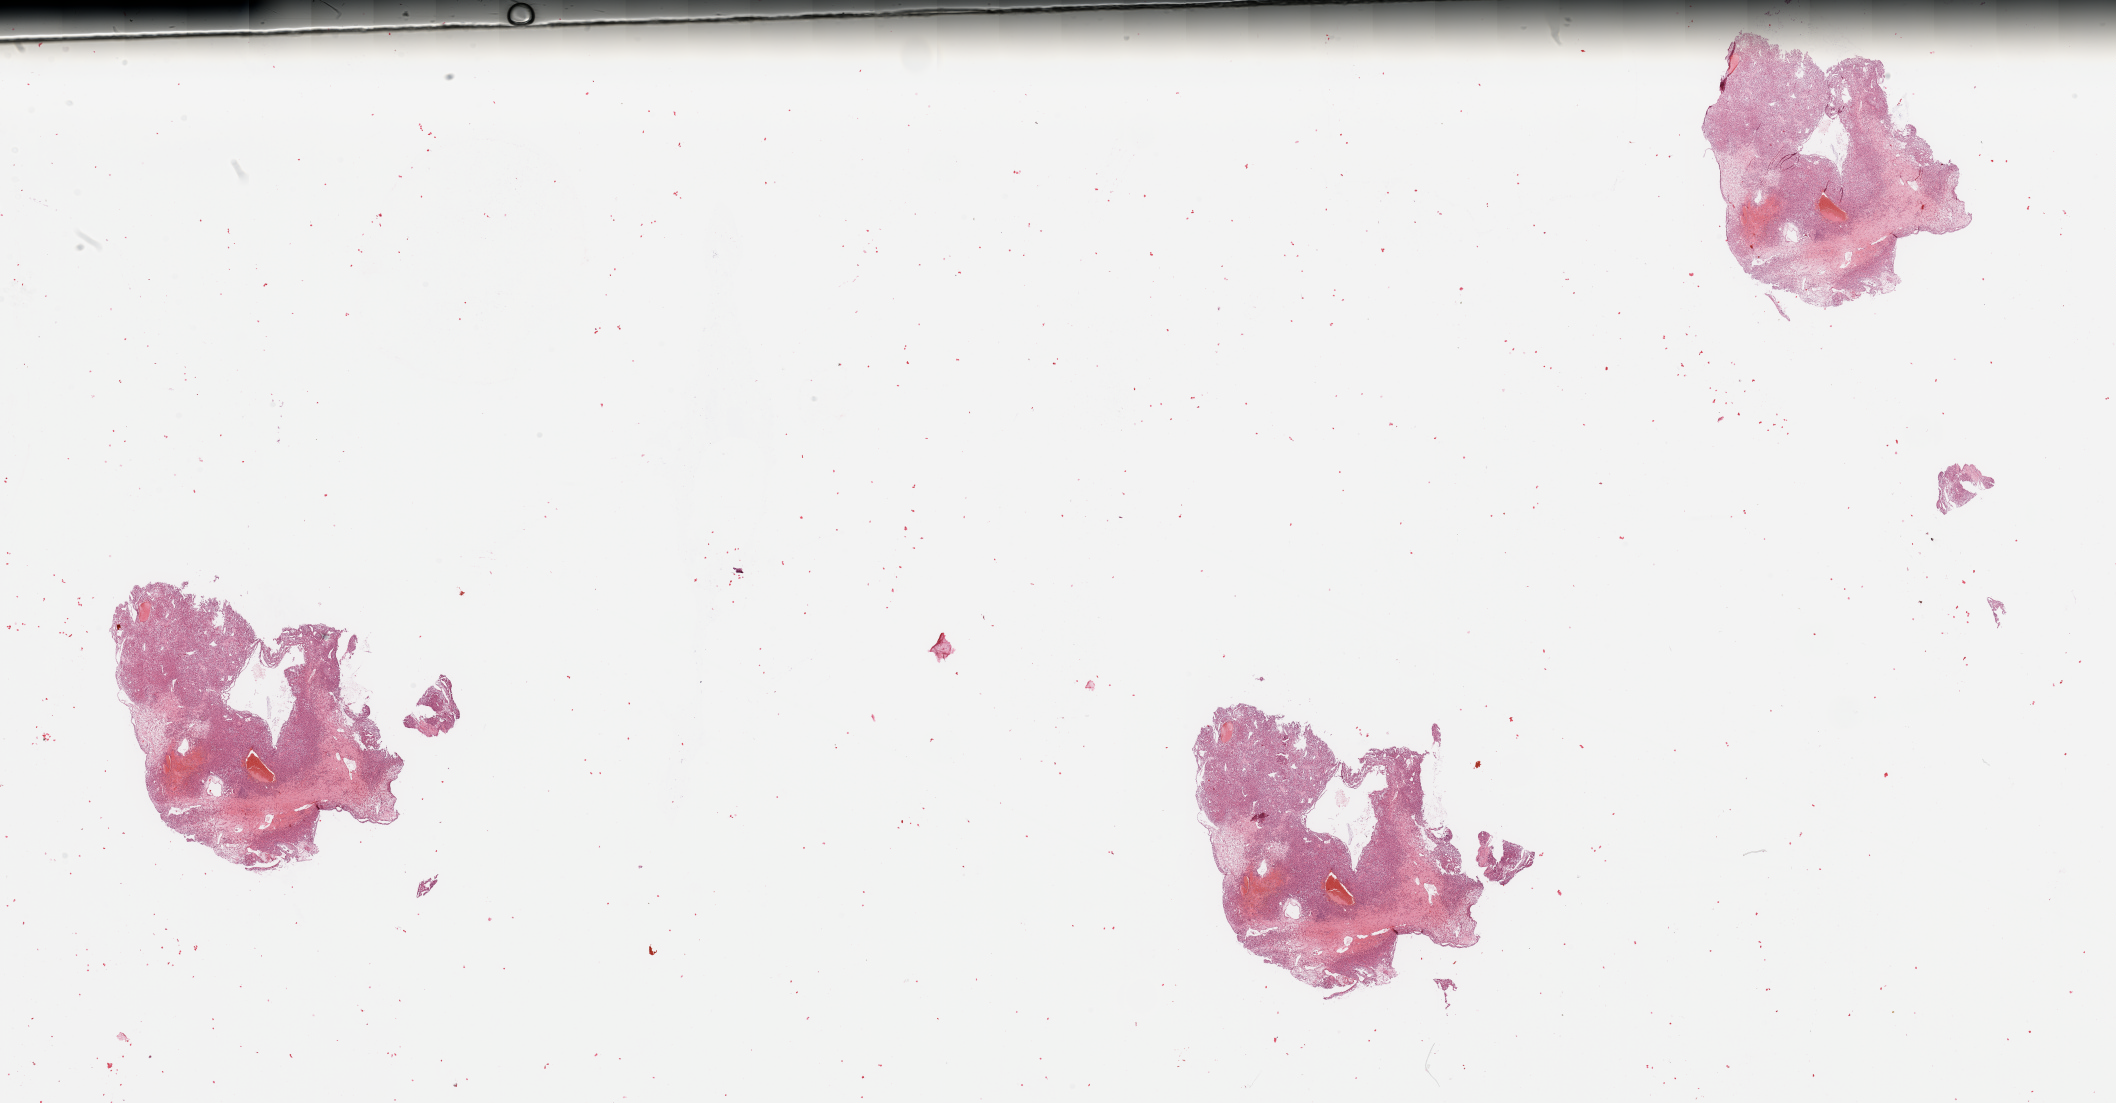
Whole-slide histology image, Hematoxylin and eosin (H&E) stained — a low-resolution overview of the entire scanned area, about 33.5 x 17.4 mm. Tumour tissue sample, sampled site: kidney. Patient: female, age 55 years. Slide review estimates, as recorded: tumour nuclei 80%, necrosis 5%.
Diagnosis: Renal cell carcinoma, NOS.